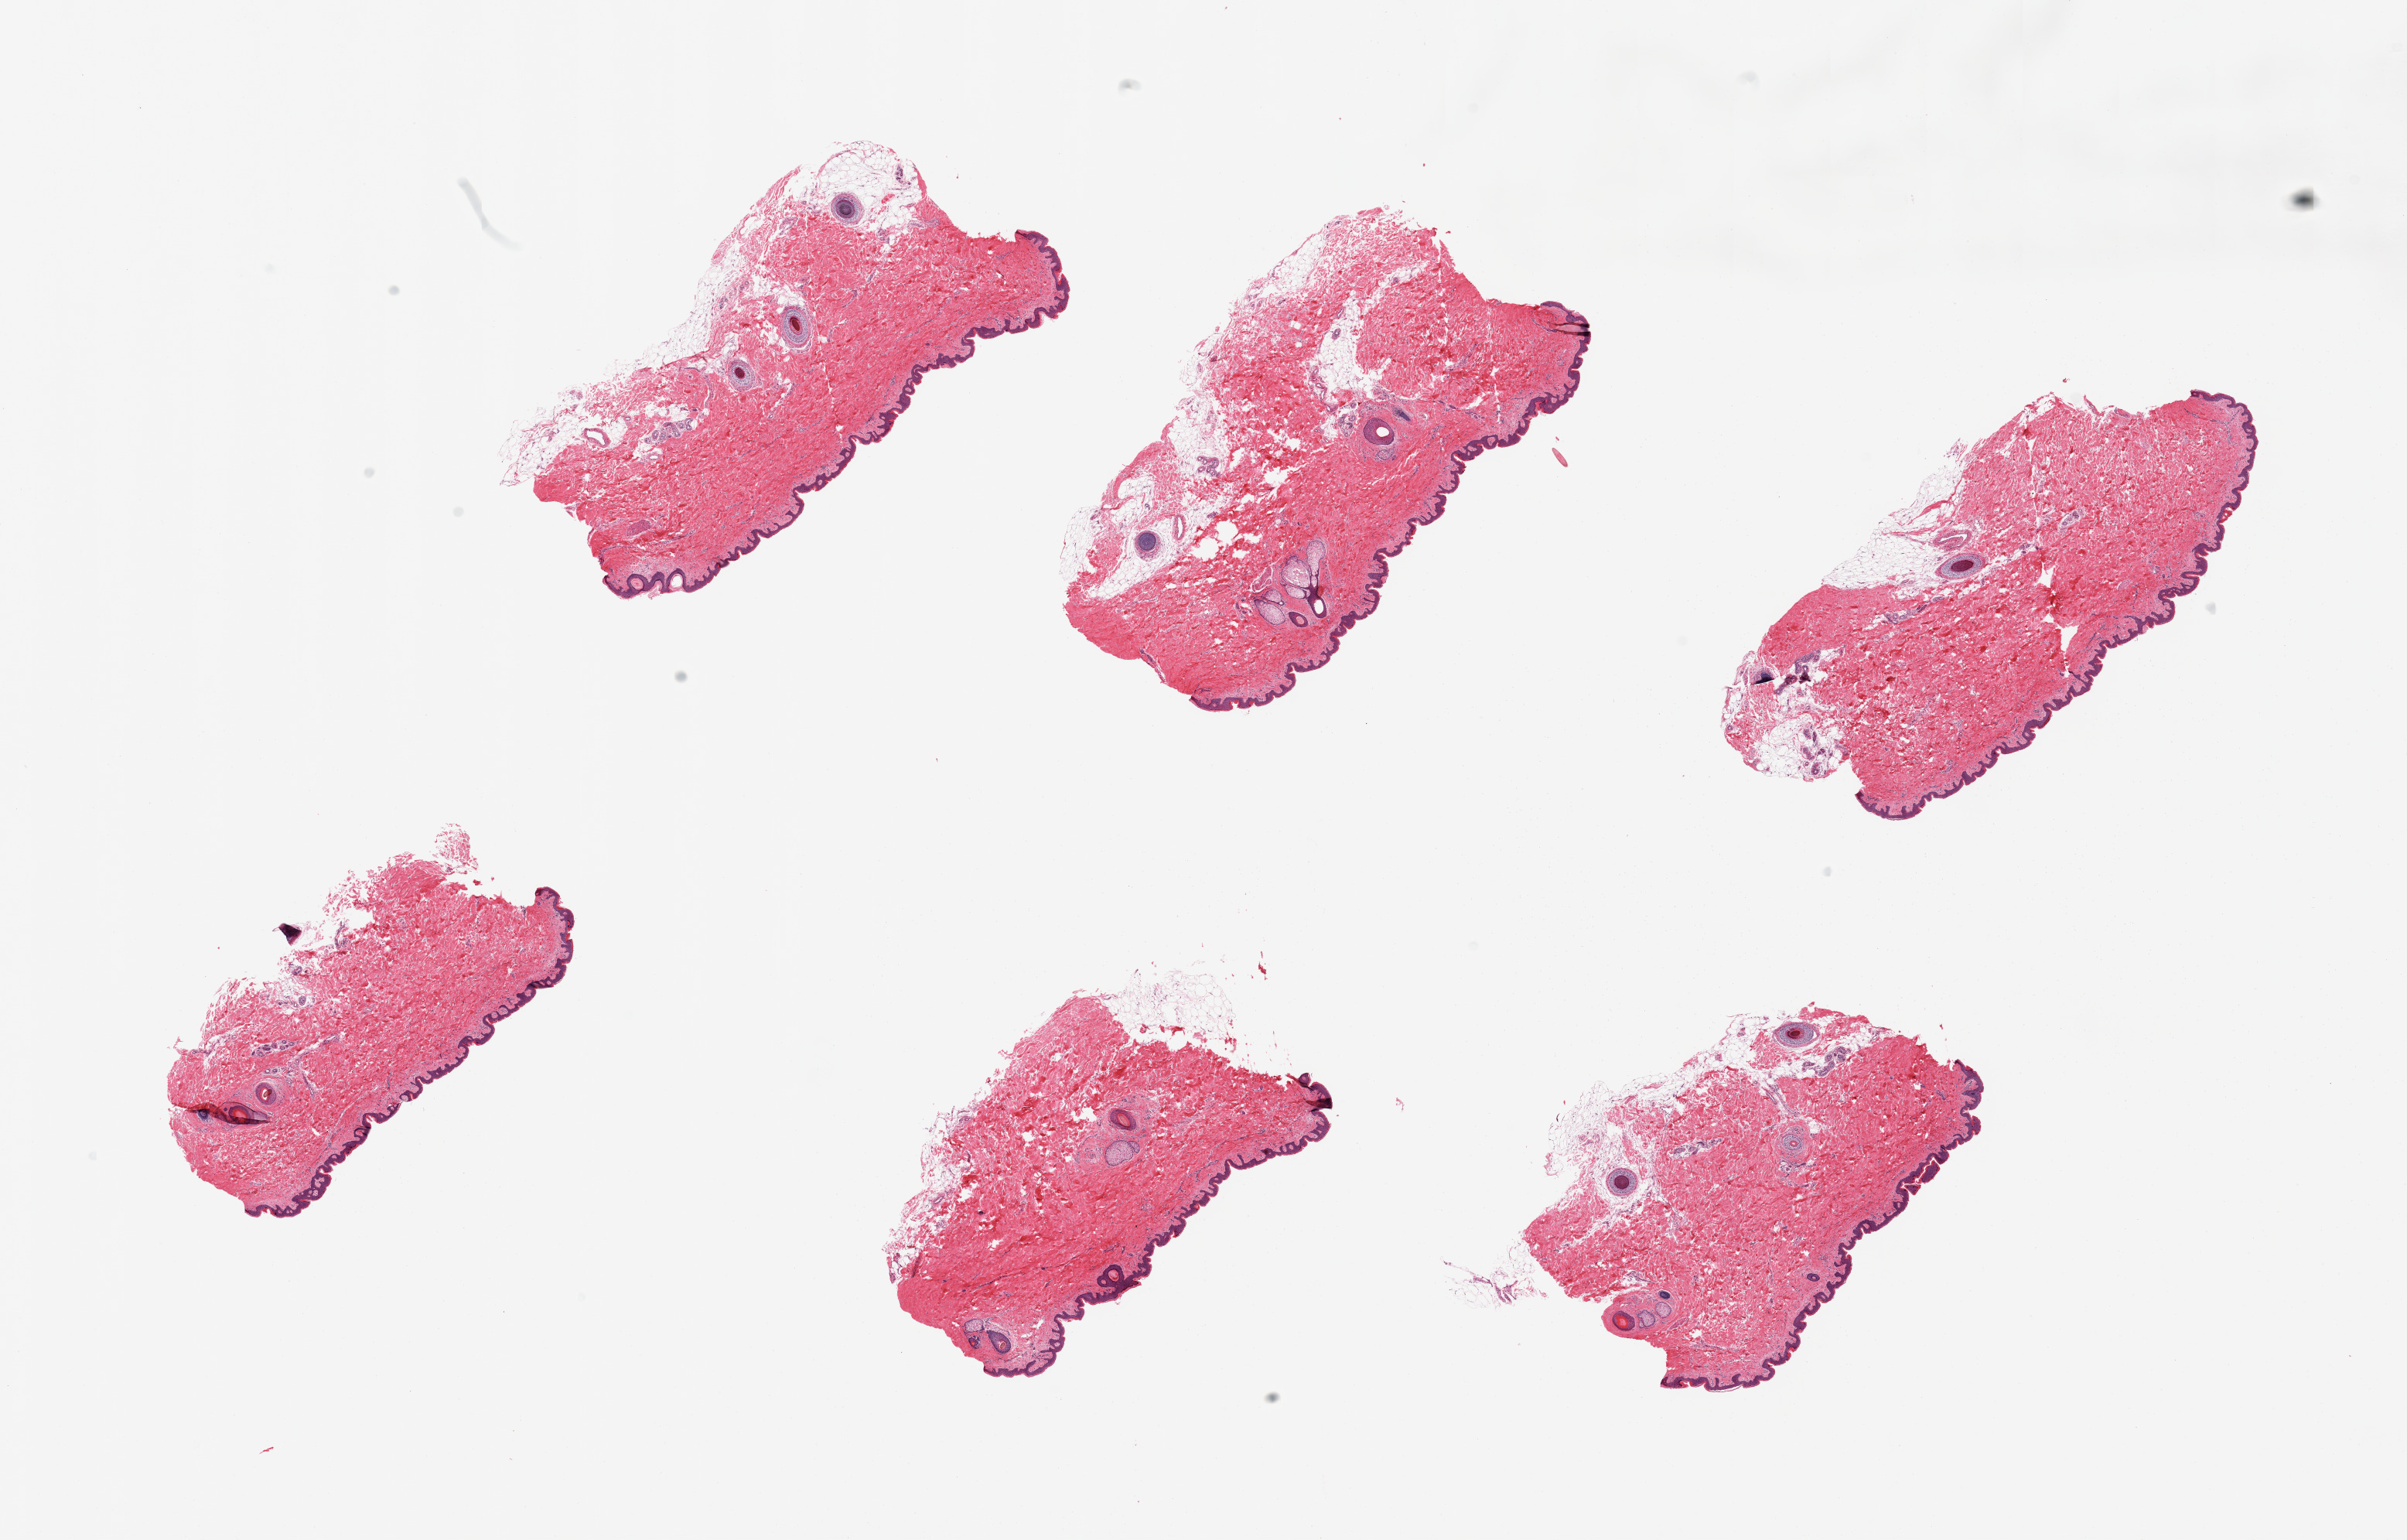
Haematoxylin and eosin whole-slide image, brightfield, a low-resolution overview of the entire scanned area, about 24.6 x 15.7 mm. PAXgene-fixed, paraffin-embedded tissue. Section of skin of suprapubic region (target tissue). Tissue donor sample. Donor sex: male.
Pathologist's review note for this sample: 6 pieces; 5-10% intradermal fat.